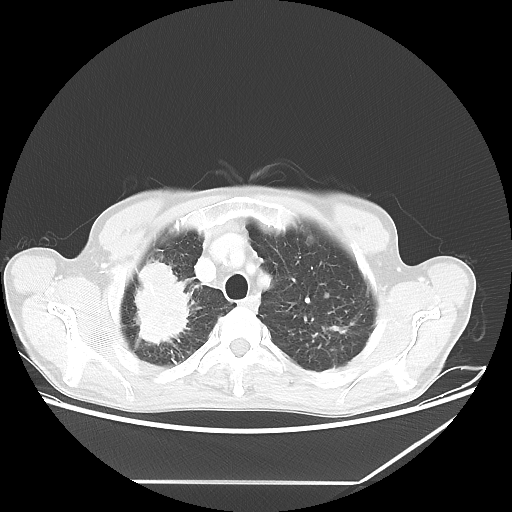
Chest CT, one axial slice. Slice 53 of 65 in the series (ordered by position). 80 kVp. Lung window (W 1500 / L -600 HU). 5 mm slice thickness. 512 × 512 image matrix, field of view 397 × 397 mm. Patient: male, 68 years. From the clinical record (not read from this slice): clinical TNM (as recorded): T3 N3 M0.
Annotated regions visible in this slice (rectangle marked by the reading radiologist):
- lung tumour (recorded histology: adenocarcinoma): bounding box [x1, y1, x2, y2] px = [113, 259, 188, 354]